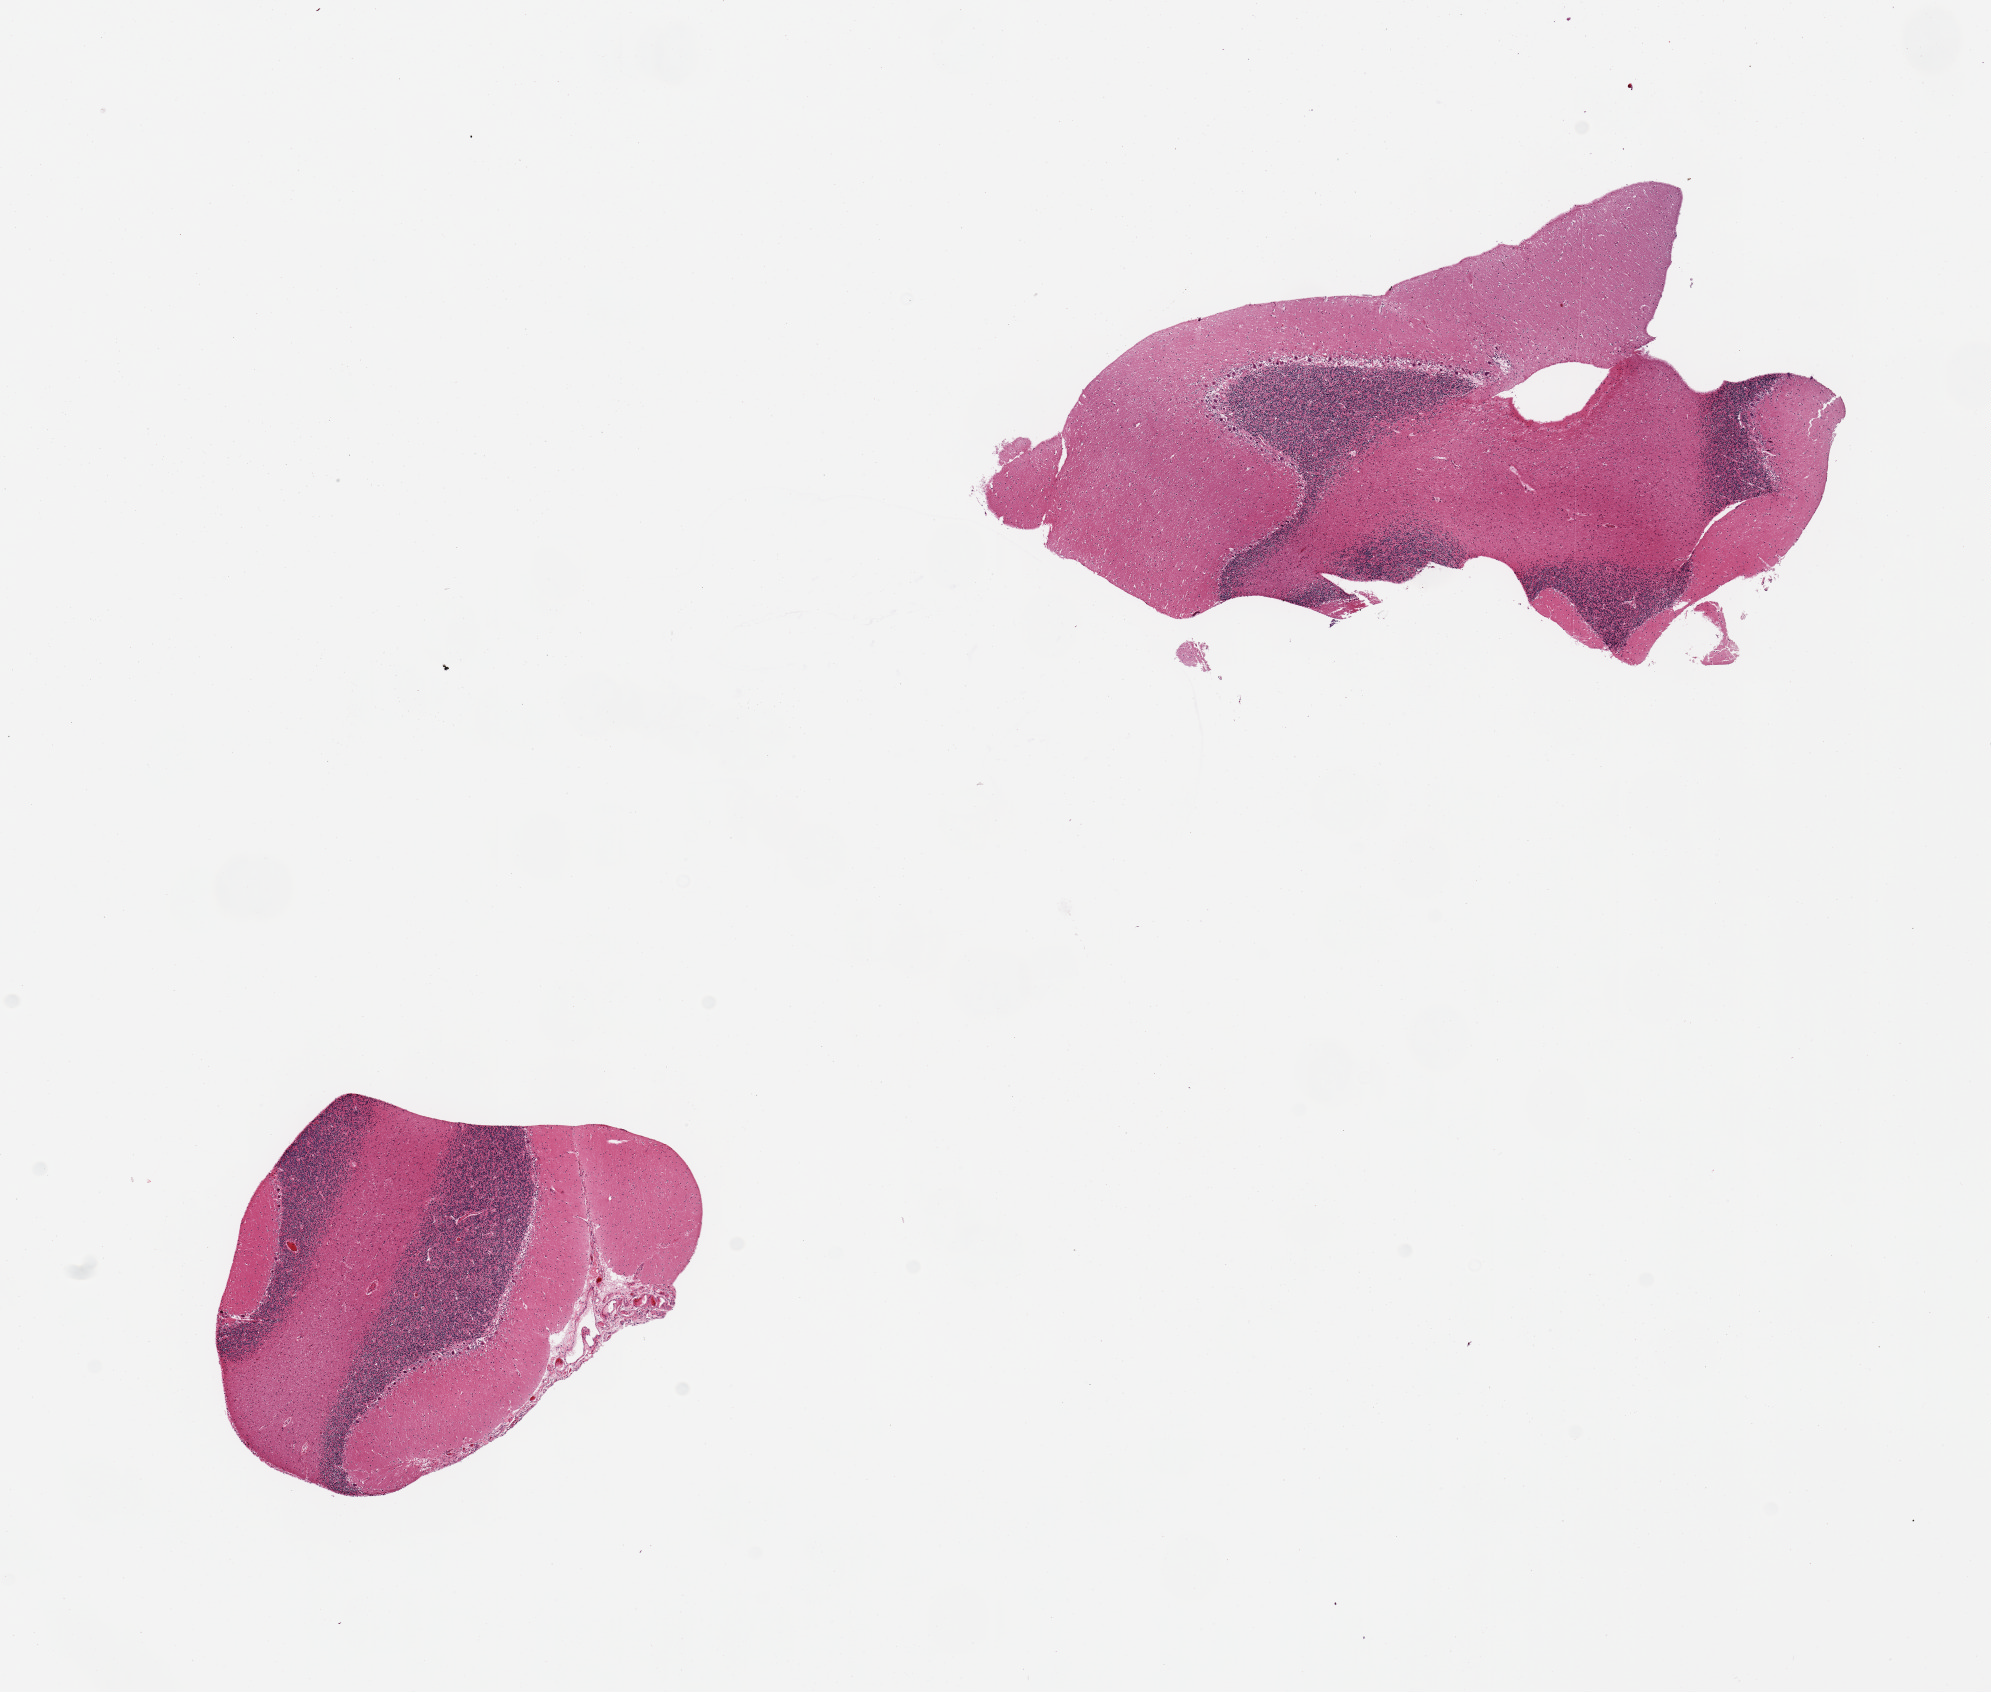
Hematoxylin and eosin (H&E) whole-slide image, shown as a low-resolution overview of the whole scanned area (about 15.8 x 13.4 mm). PAXgene-fixed, paraffin-embedded tissue. Target tissue: cerebellum. Tissue donor sample. Donor sex: male.
Pathologist's review note for this sample: 2 pieces.